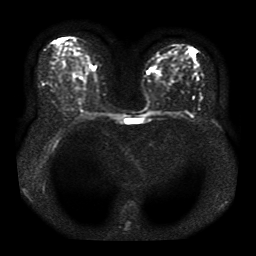
Breast MRI, one axial slice; slice 18 of 41 in the series (ordered by position); diffusion-weighted series; image 2 of 4 stored at this slice position (different b-values; order by instance number); 1.5 T; 5 mm slice thickness; 256 × 256 image matrix. Female patient.
Structures marked on this image (manually delineated by an expert):
- tumour on diffusion-weighted imaging: bounding box <77,65,89,76> (left, top, right, bottom; pixels)